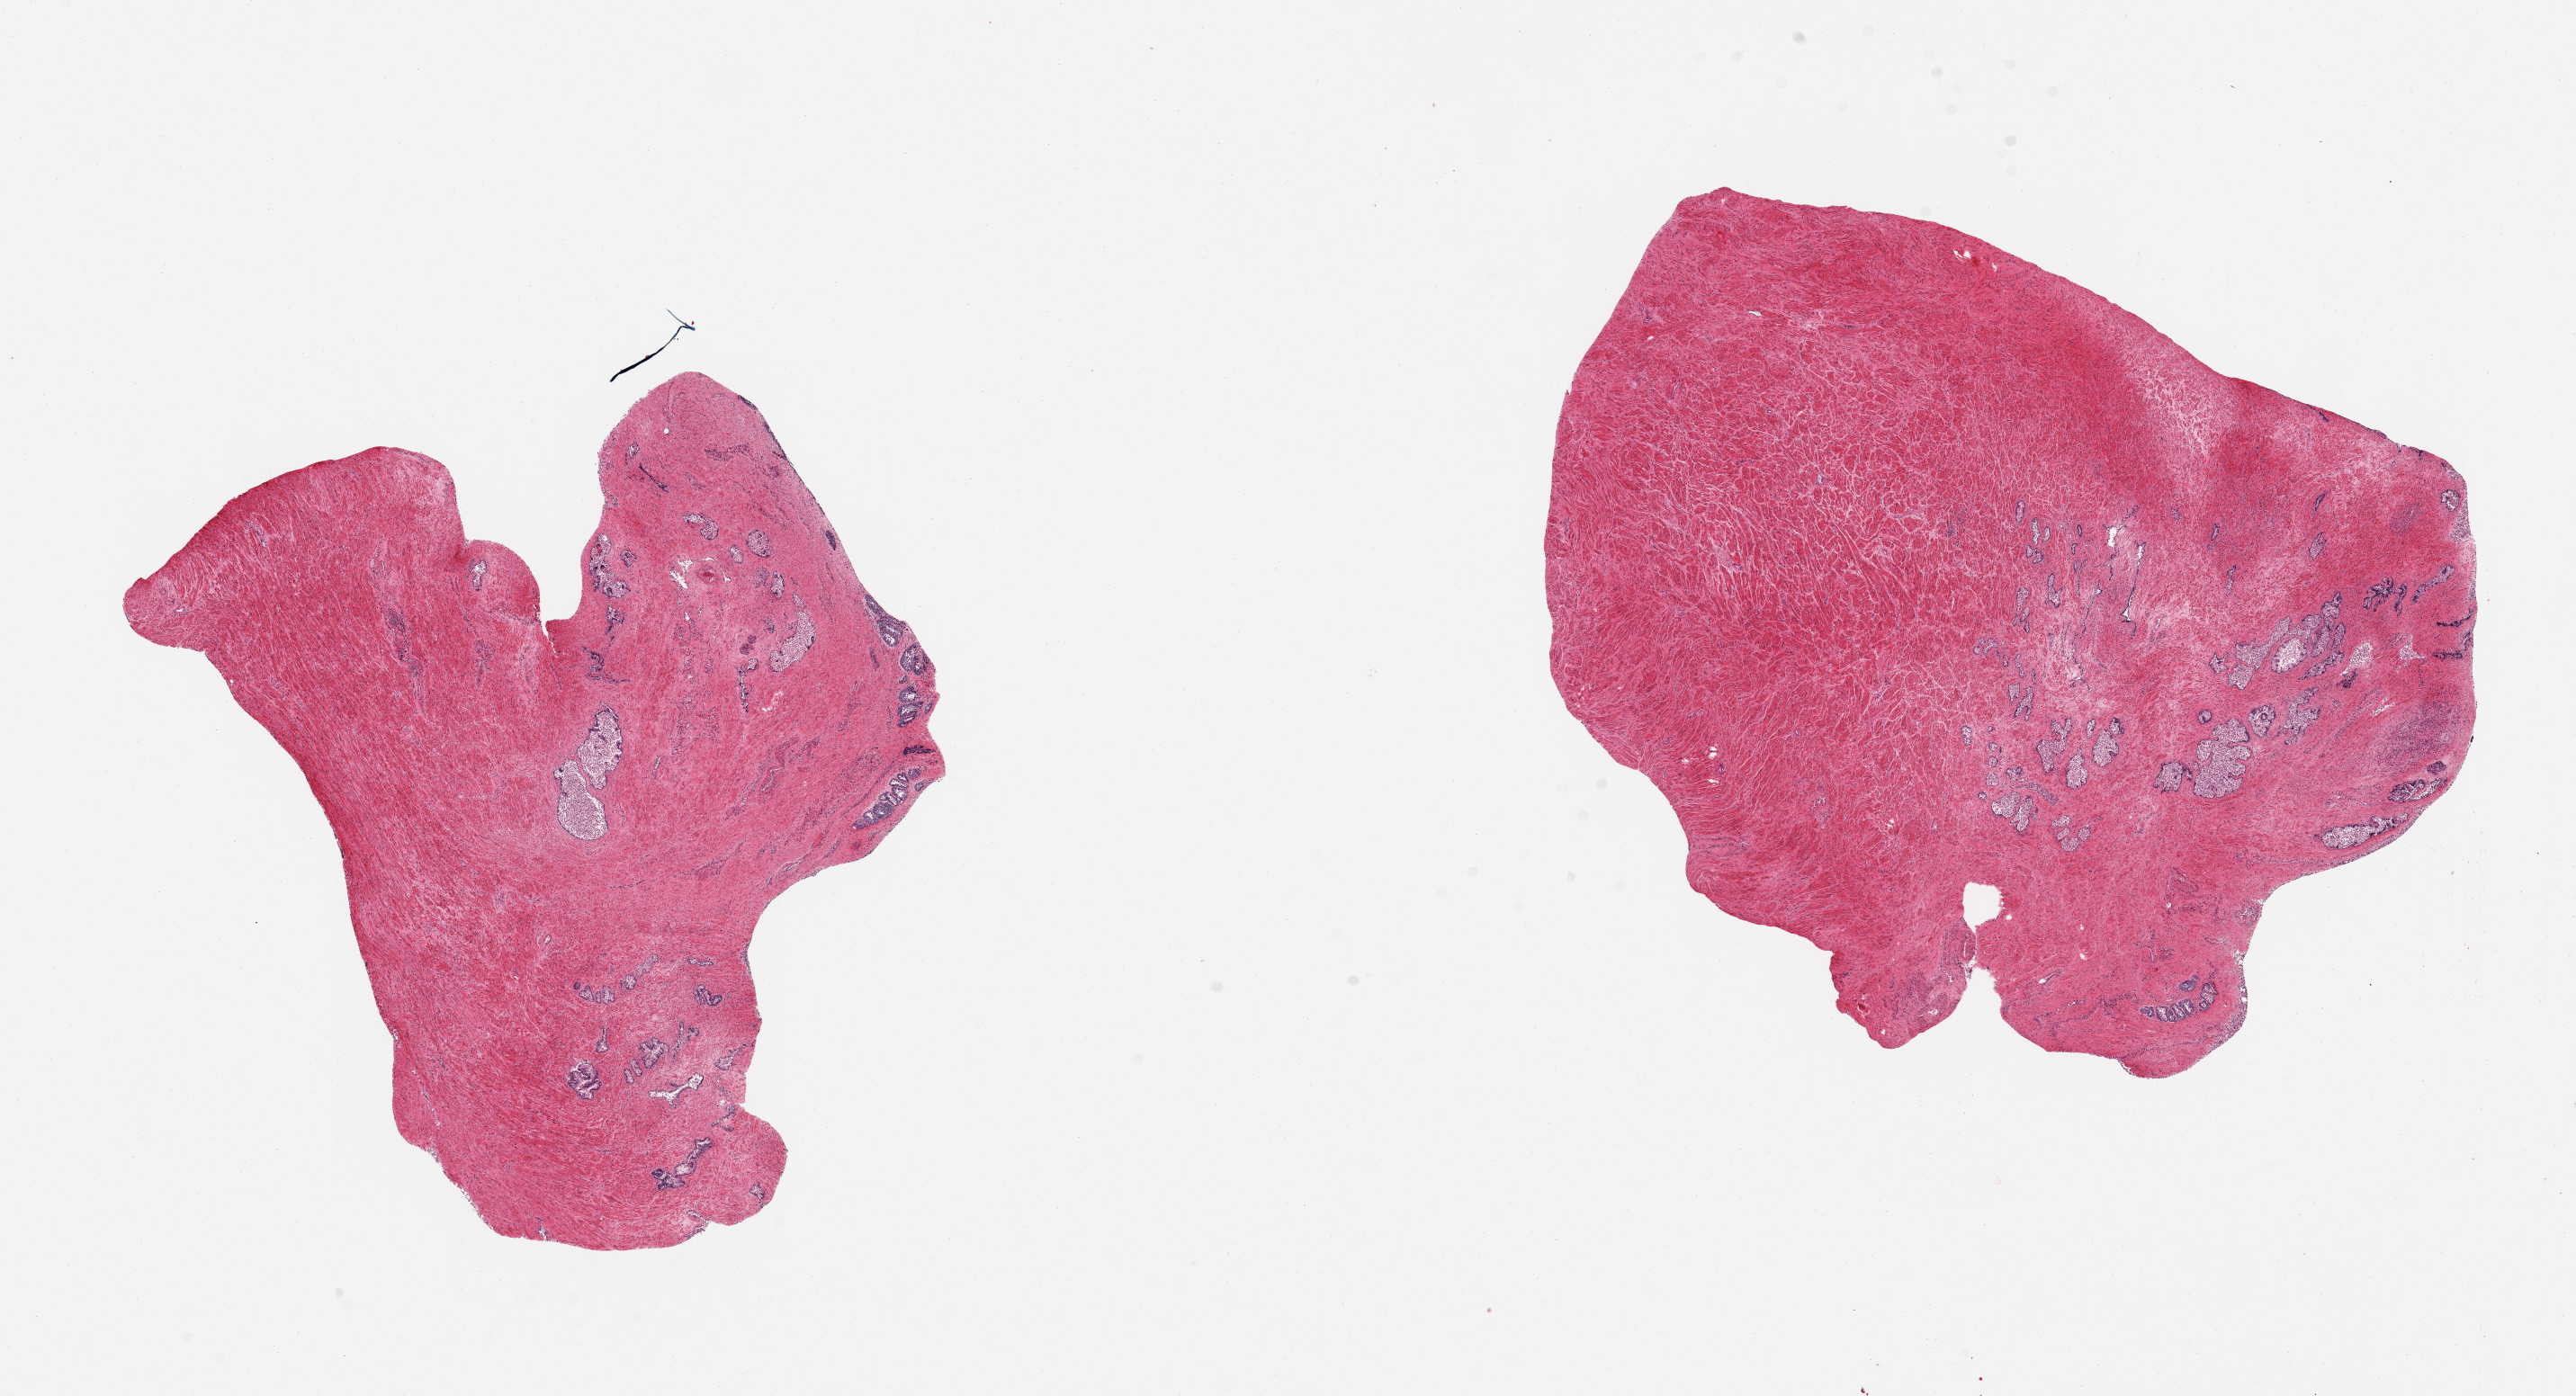
Digitized H&E-stained section, whole scanned area (about 22.6 x 12.3 mm) shown as a low-resolution overview; PAXgene-fixed, paraffin-embedded tissue; sampled site (target tissue): prostate; tissue donor sample. Donor: male.
Pathologist's review note for this sample: 2 pieces, glandular elements moderately-markedly autolyzed.